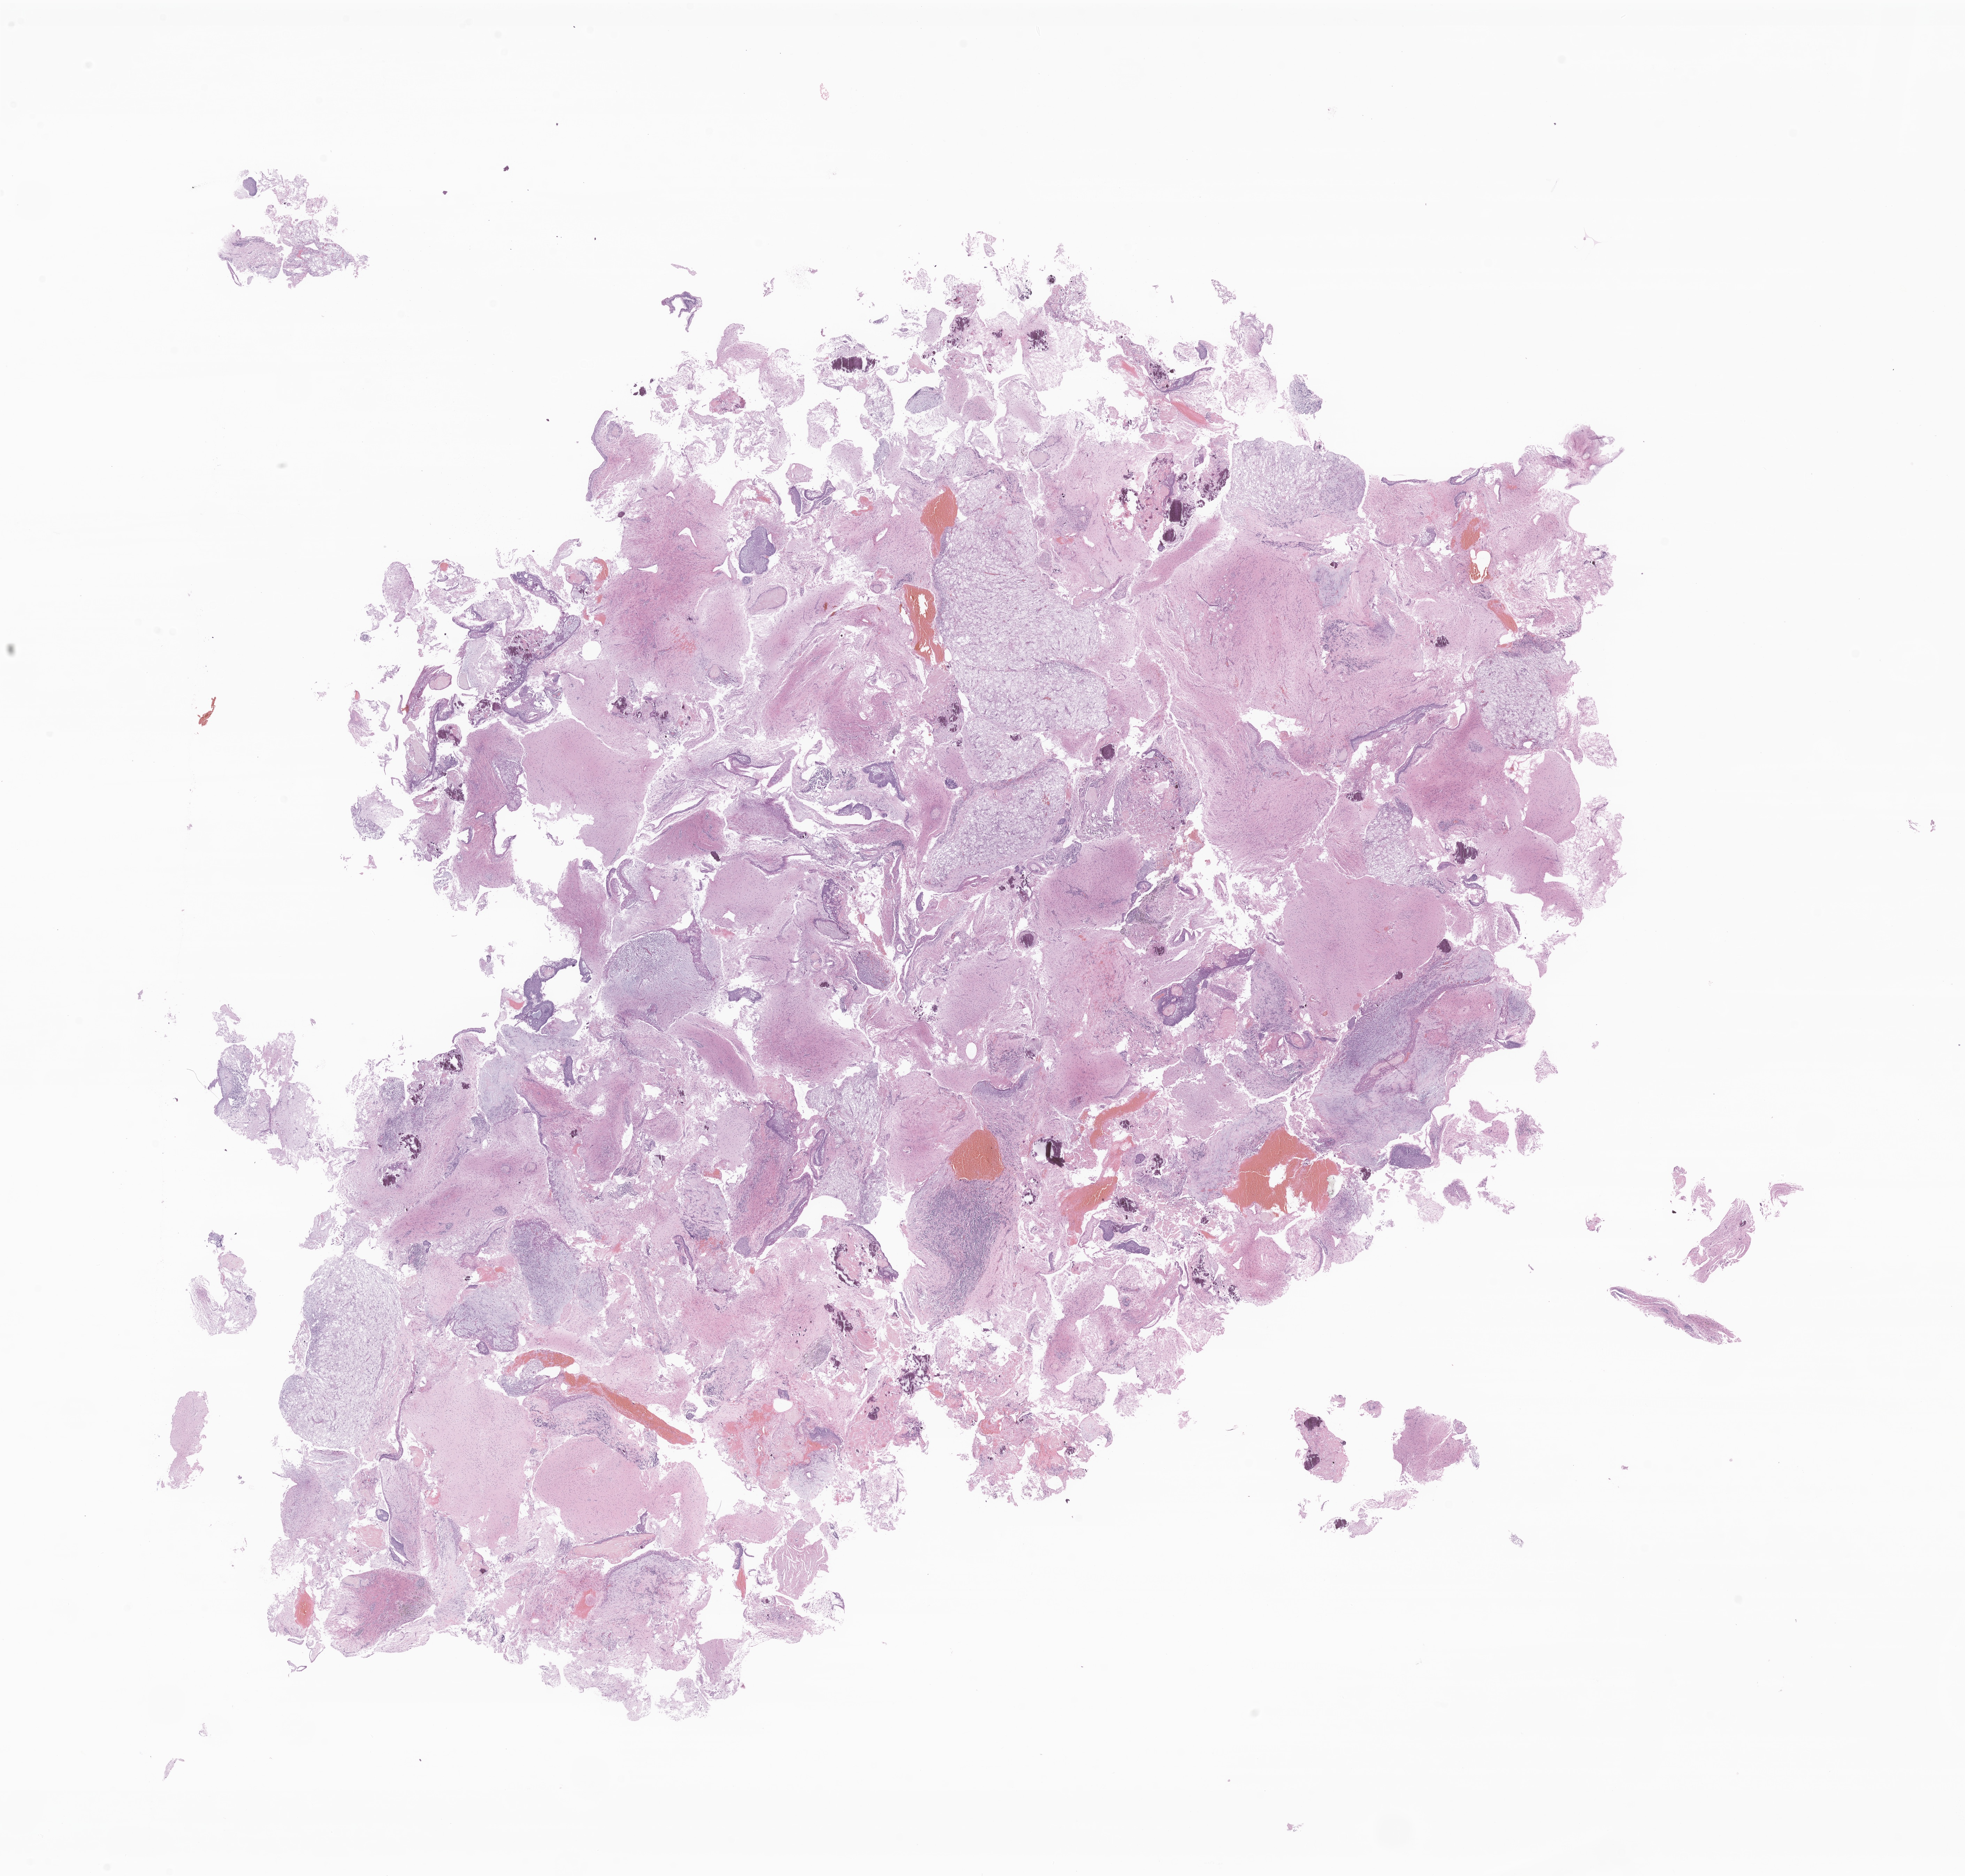
Whole-slide image, H&E stain of tumor tissue from the brain, shown as a low-resolution overview of the whole scanned area (about 23.8 x 22.7 mm), FFPE section. Female patient, age 121 months.
Recorded diagnosis: Craniopharyngioma, NOS.